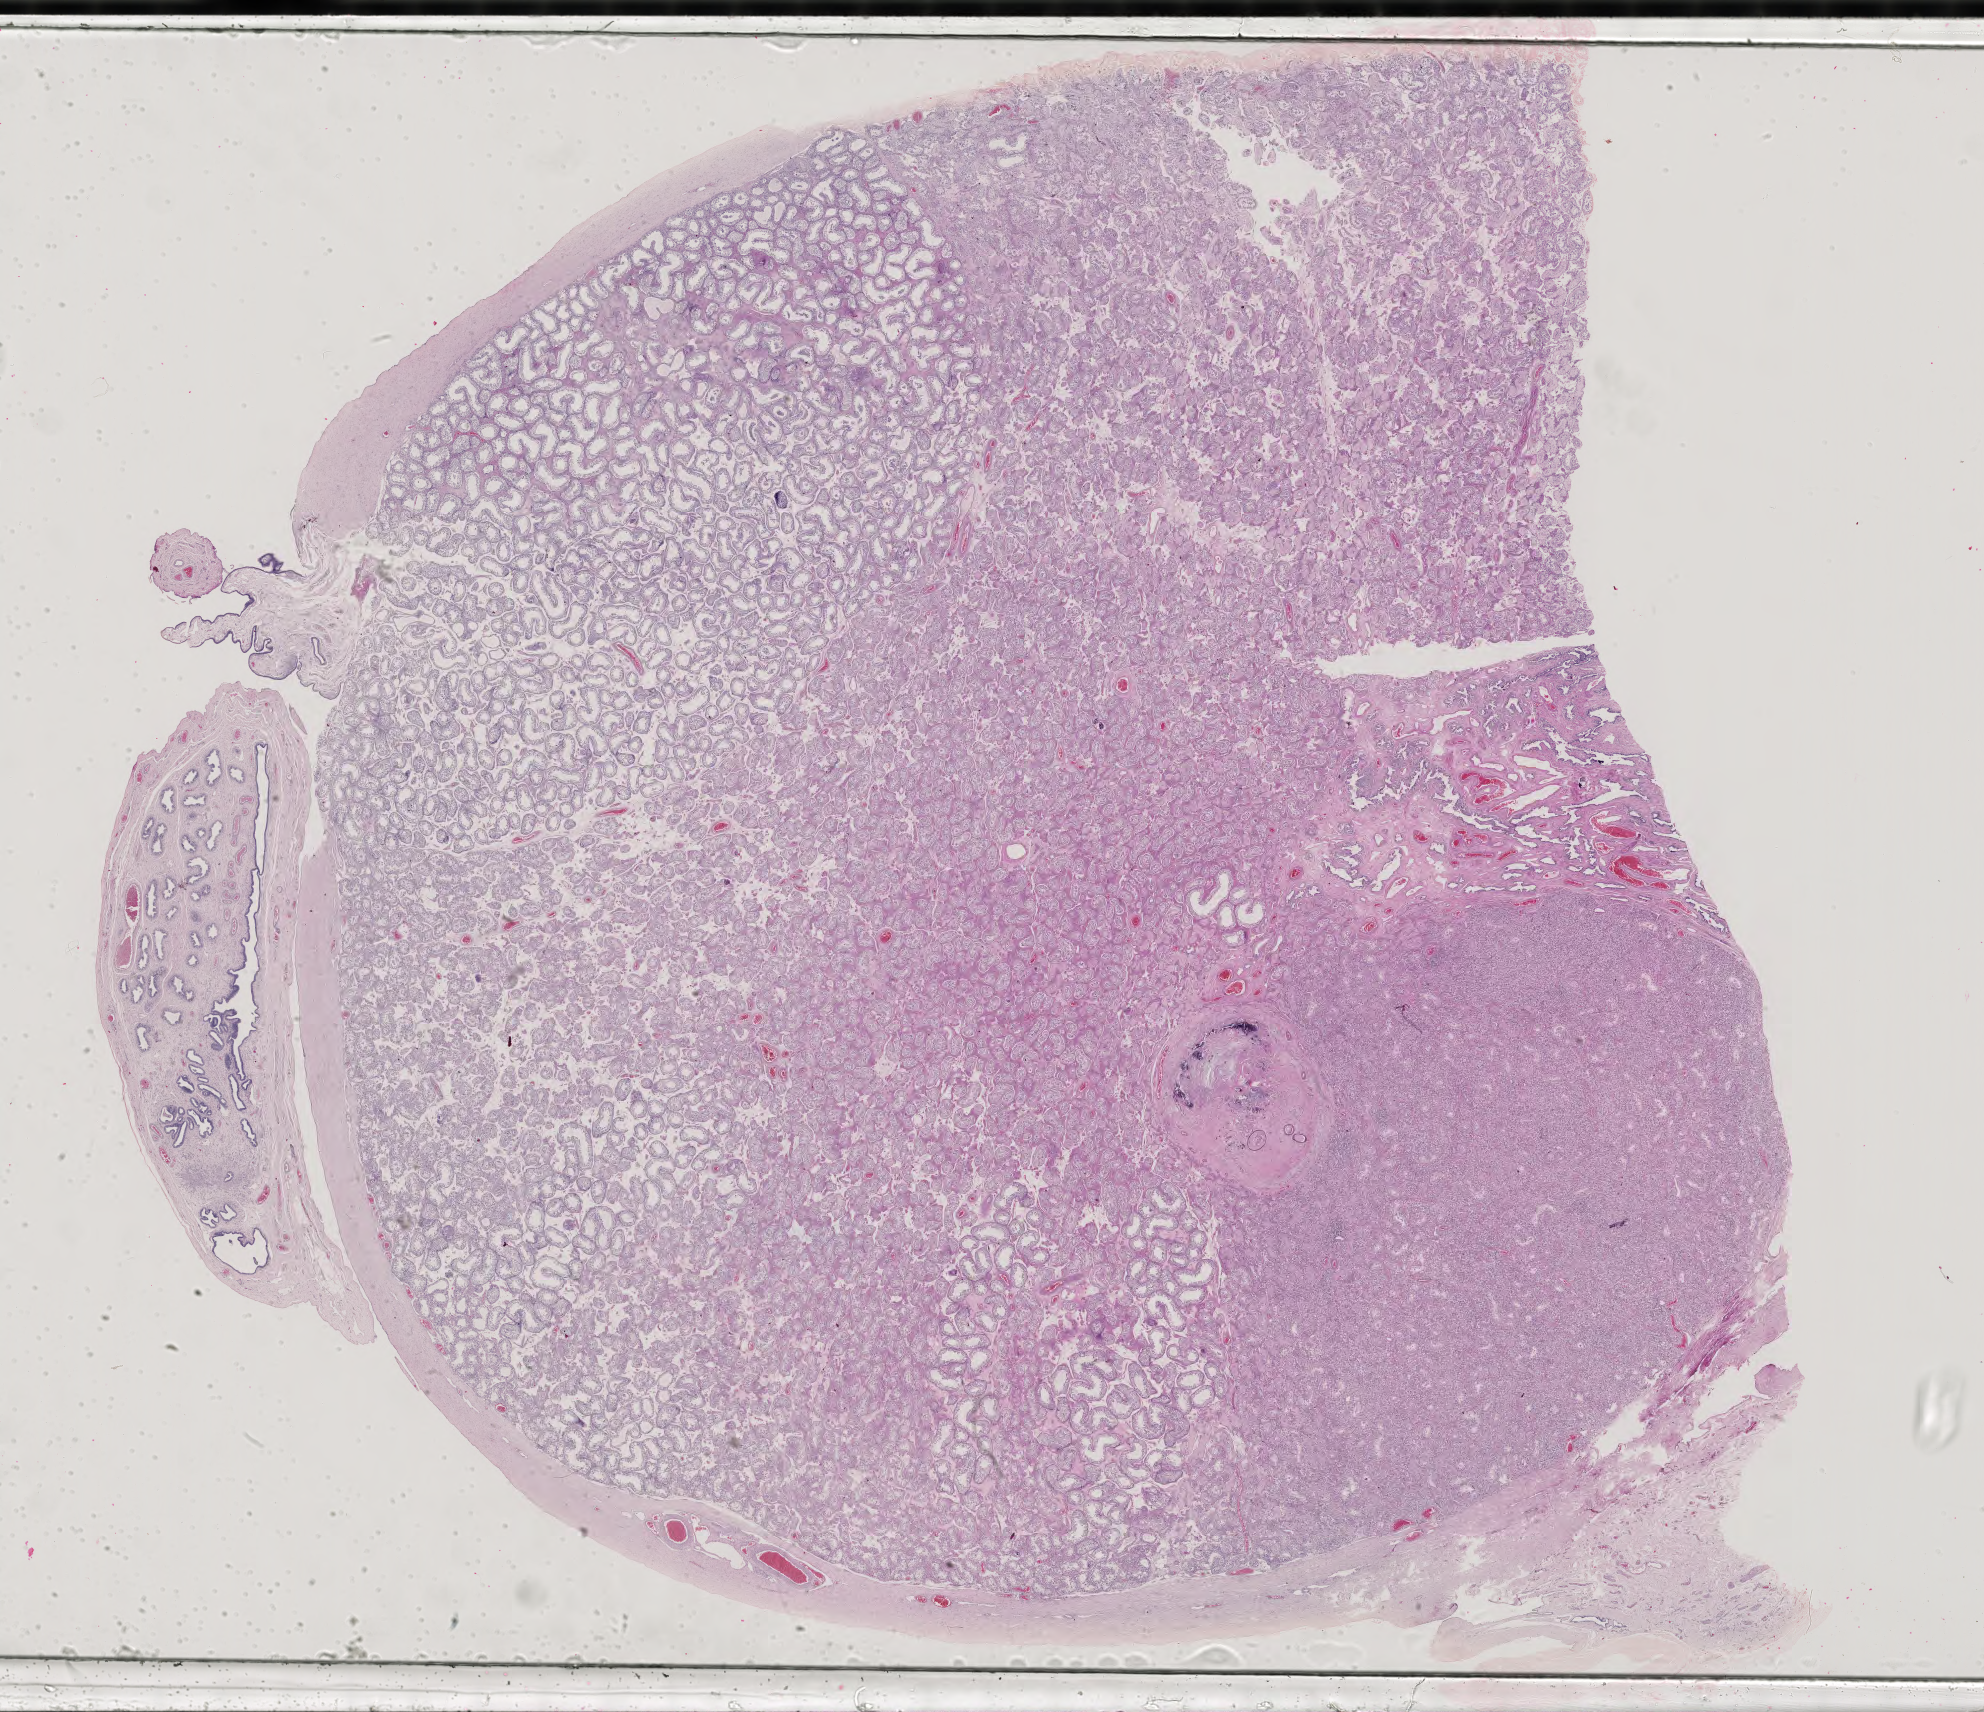
Digitized H&E tissue section (whole slide) — whole scanned area (about 28.9 x 24.9 mm) shown as a low-resolution overview. Formalin-fixed paraffin-embedded (FFPE) diagnostic section. Sample: additional new primary tumour, testis. Patient: male, age at initial diagnosis 28 years.
This section: additional new primary tumour. Patient diagnosis: Teratoma, benign.